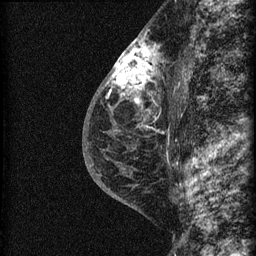
Breast MRI (dynamic contrast-enhanced), one sagittal slice; position 37 of 60 along the scan axis; dynamic contrast-enhanced series, image 2 of 3 at this slice position (ordered by acquisition); 1.5 T; TE 4.2 ms, TR 22.7 ms; 1.5 mm slice thickness; 256 × 256 image matrix, field of view 180 × 180 mm. Female patient, age 48 years. Case-level facts recorded for this patient, not image findings: setting: breast cancer imaged before/during neoadjuvant chemotherapy; receptor status: triple-negative.
Outlined on this slice (semi-automatically segmented with operator editing):
- analysis volume of interest (the breast-tissue region the enhancement analysis was run in; not a lesion): bounding box <115,34,169,162> (left, top, right, bottom; pixels)
- tumour enhancement mask (voxels above the 90 % enhancement threshold inside the analysis volume of interest): <115,35,157,103>